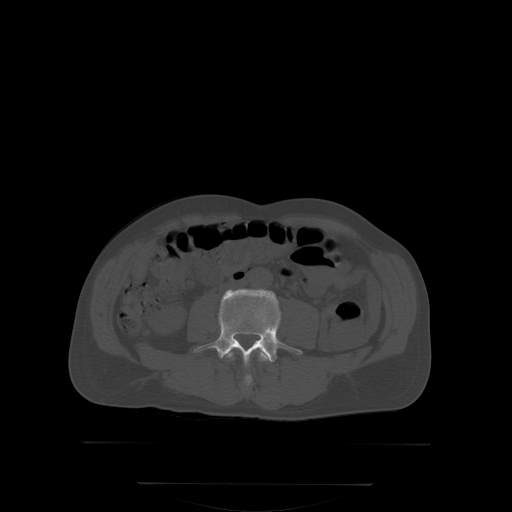
CT including the spine, one axial slice. Slice 112 of 350 in the series (ordered by position). Bone window (W 1800 / L 400 HU). 2.5 mm slice thickness. 512 × 512 image matrix. Male patient, age 58 years. From the clinical record (not read from this slice): primary cancer: prostate.
Annotated regions visible in this slice (semi-automatic segmentation, software-assisted and operator-edited):
- L3 vertebra: box from (x=228, y=352) to (x=267, y=362) px
- L4 vertebra: (x=194, y=291)–(x=302, y=384)